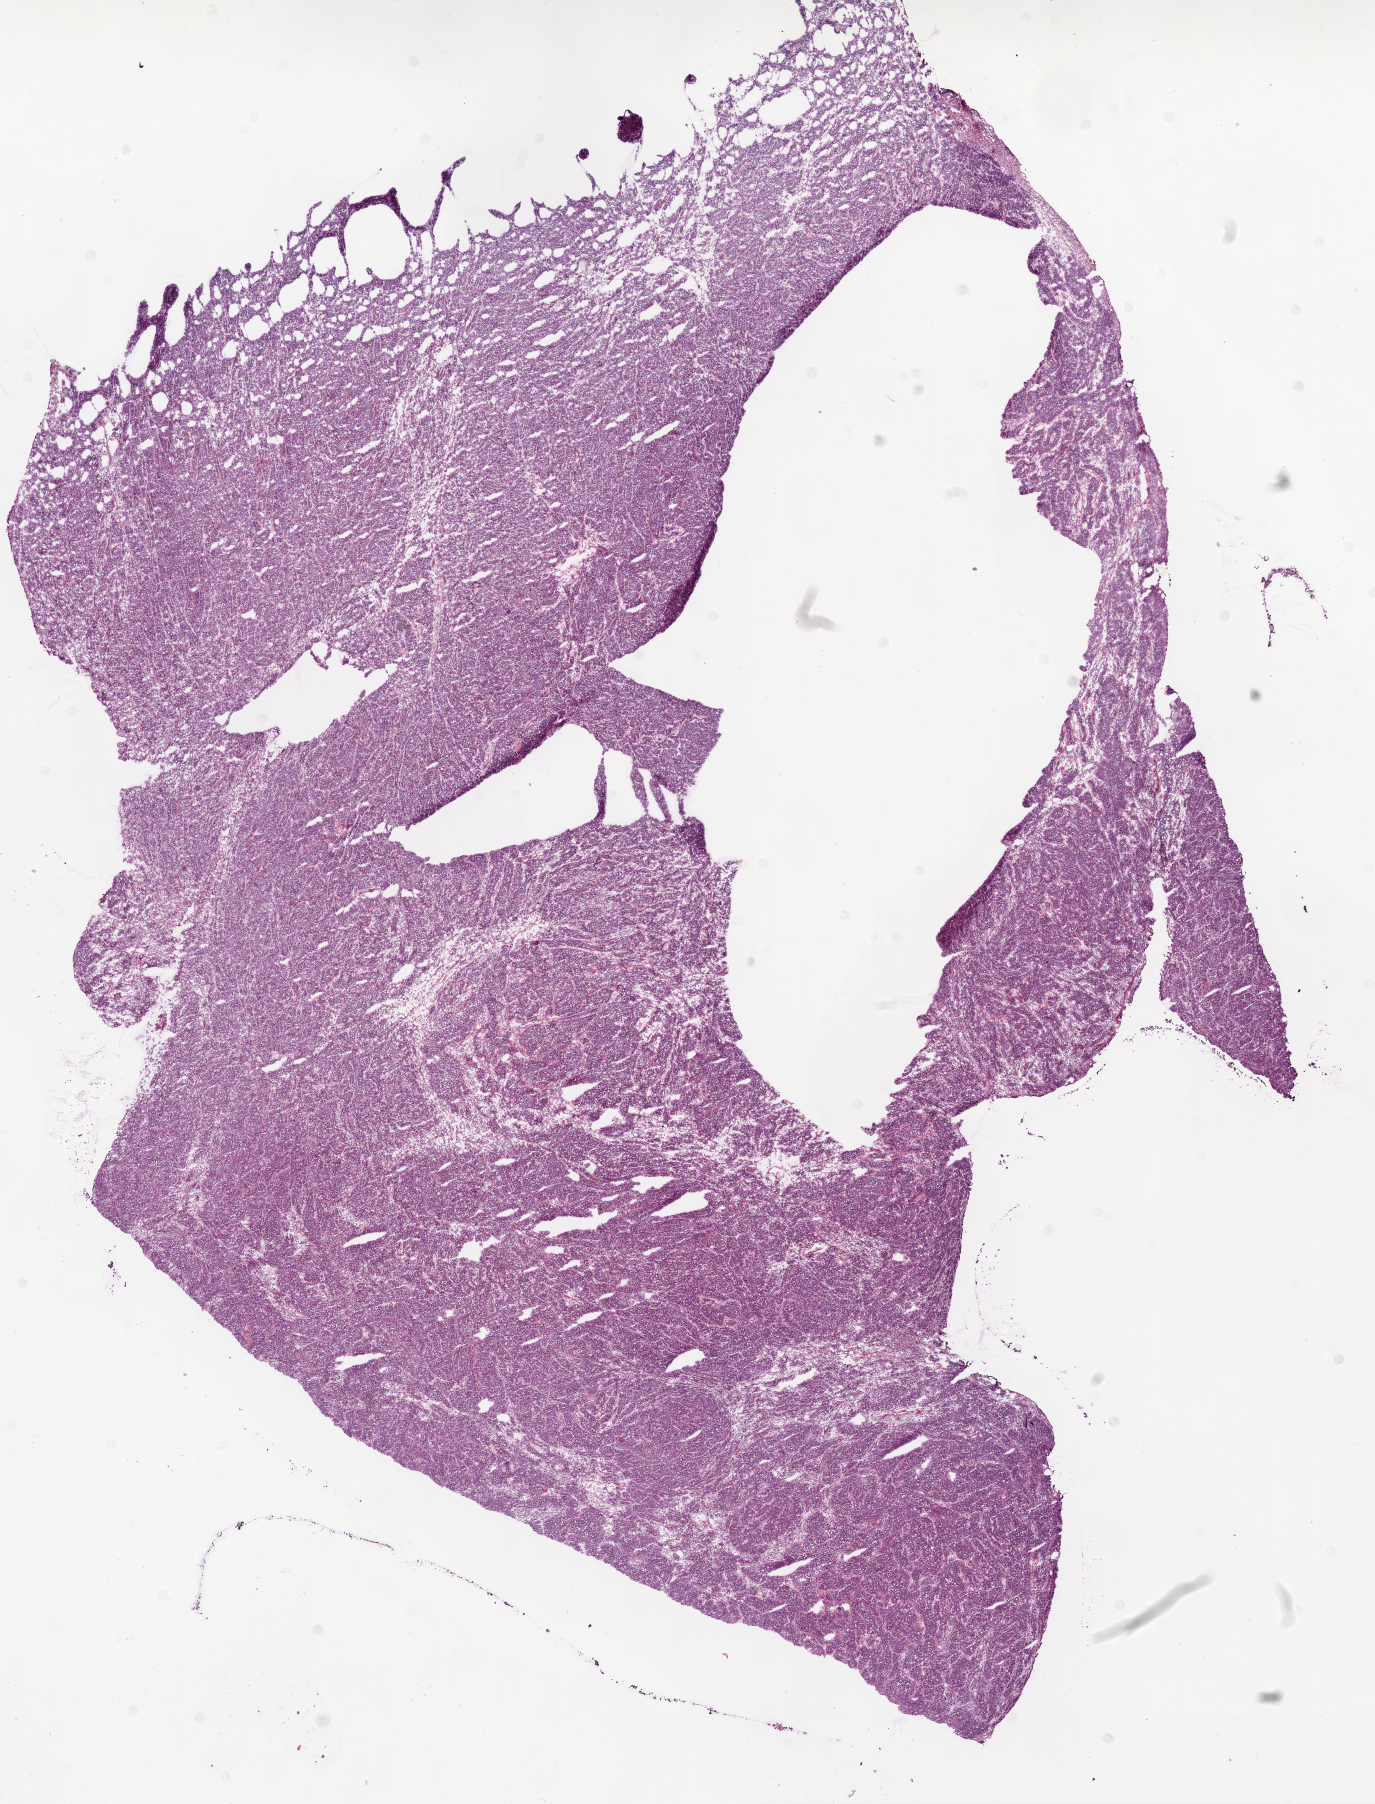
Digitized H&E tissue section (whole slide) — a low-resolution overview of the entire scanned area, about 11.0 x 14.5 mm (acquisition: 20x scan). Frozen section. Sample: primary tumour, ovary. Female patient; age at initial diagnosis 74 years. Histologic grade: G3 (poorly differentiated). Pathologist review of this section (percent, as recorded): tumour cells 98%, tumour nuclei 75%, normal cells 0%, stromal cells 0%, necrosis 2%. Inflammatory infiltration, as recorded: lymphocyte infiltration 15%.
Histologic diagnosis: Serous cystadenocarcinoma, NOS. FIGO stage: IC.